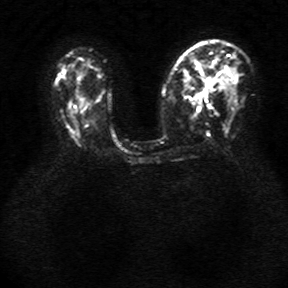
Breast MRI, one axial slice; position 19 of 34 along the scan axis; diffusion-weighted series; image 2 of 4 stored at this slice position (different b-values; order by instance number); 1.5 T; 5 mm slice thickness; 288 × 288 image matrix, field of view 340 × 340 mm. Female patient.
Structures marked on this image (manually delineated by an expert):
- tumour on diffusion-weighted imaging: bounding box <203,78,211,98> (left, top, right, bottom; pixels)